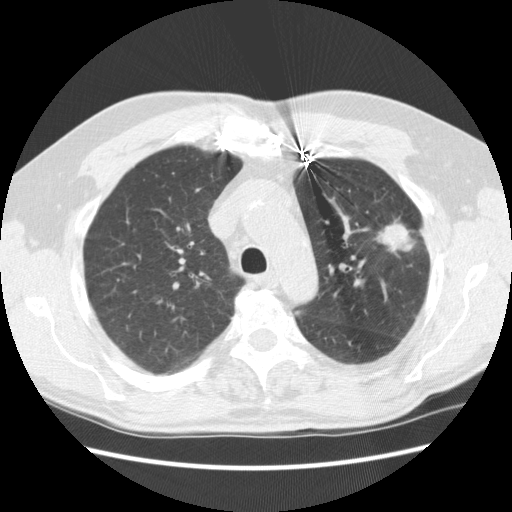
Low-dose screening chest CT, one axial slice; slice 176 of 231 in the series (ordered by position); reconstruction kernel STANDARD; lung window (W 1500 / L -600 HU); 2.5 mm slice thickness; 512 × 512 image matrix, field of view 362 × 362 mm.
Outlined on this slice (manually delineated by an expert):
- lesion 1 (tumor, upper lobe of left lung): bounding box <377,220,415,252> (left, top, right, bottom; pixels)